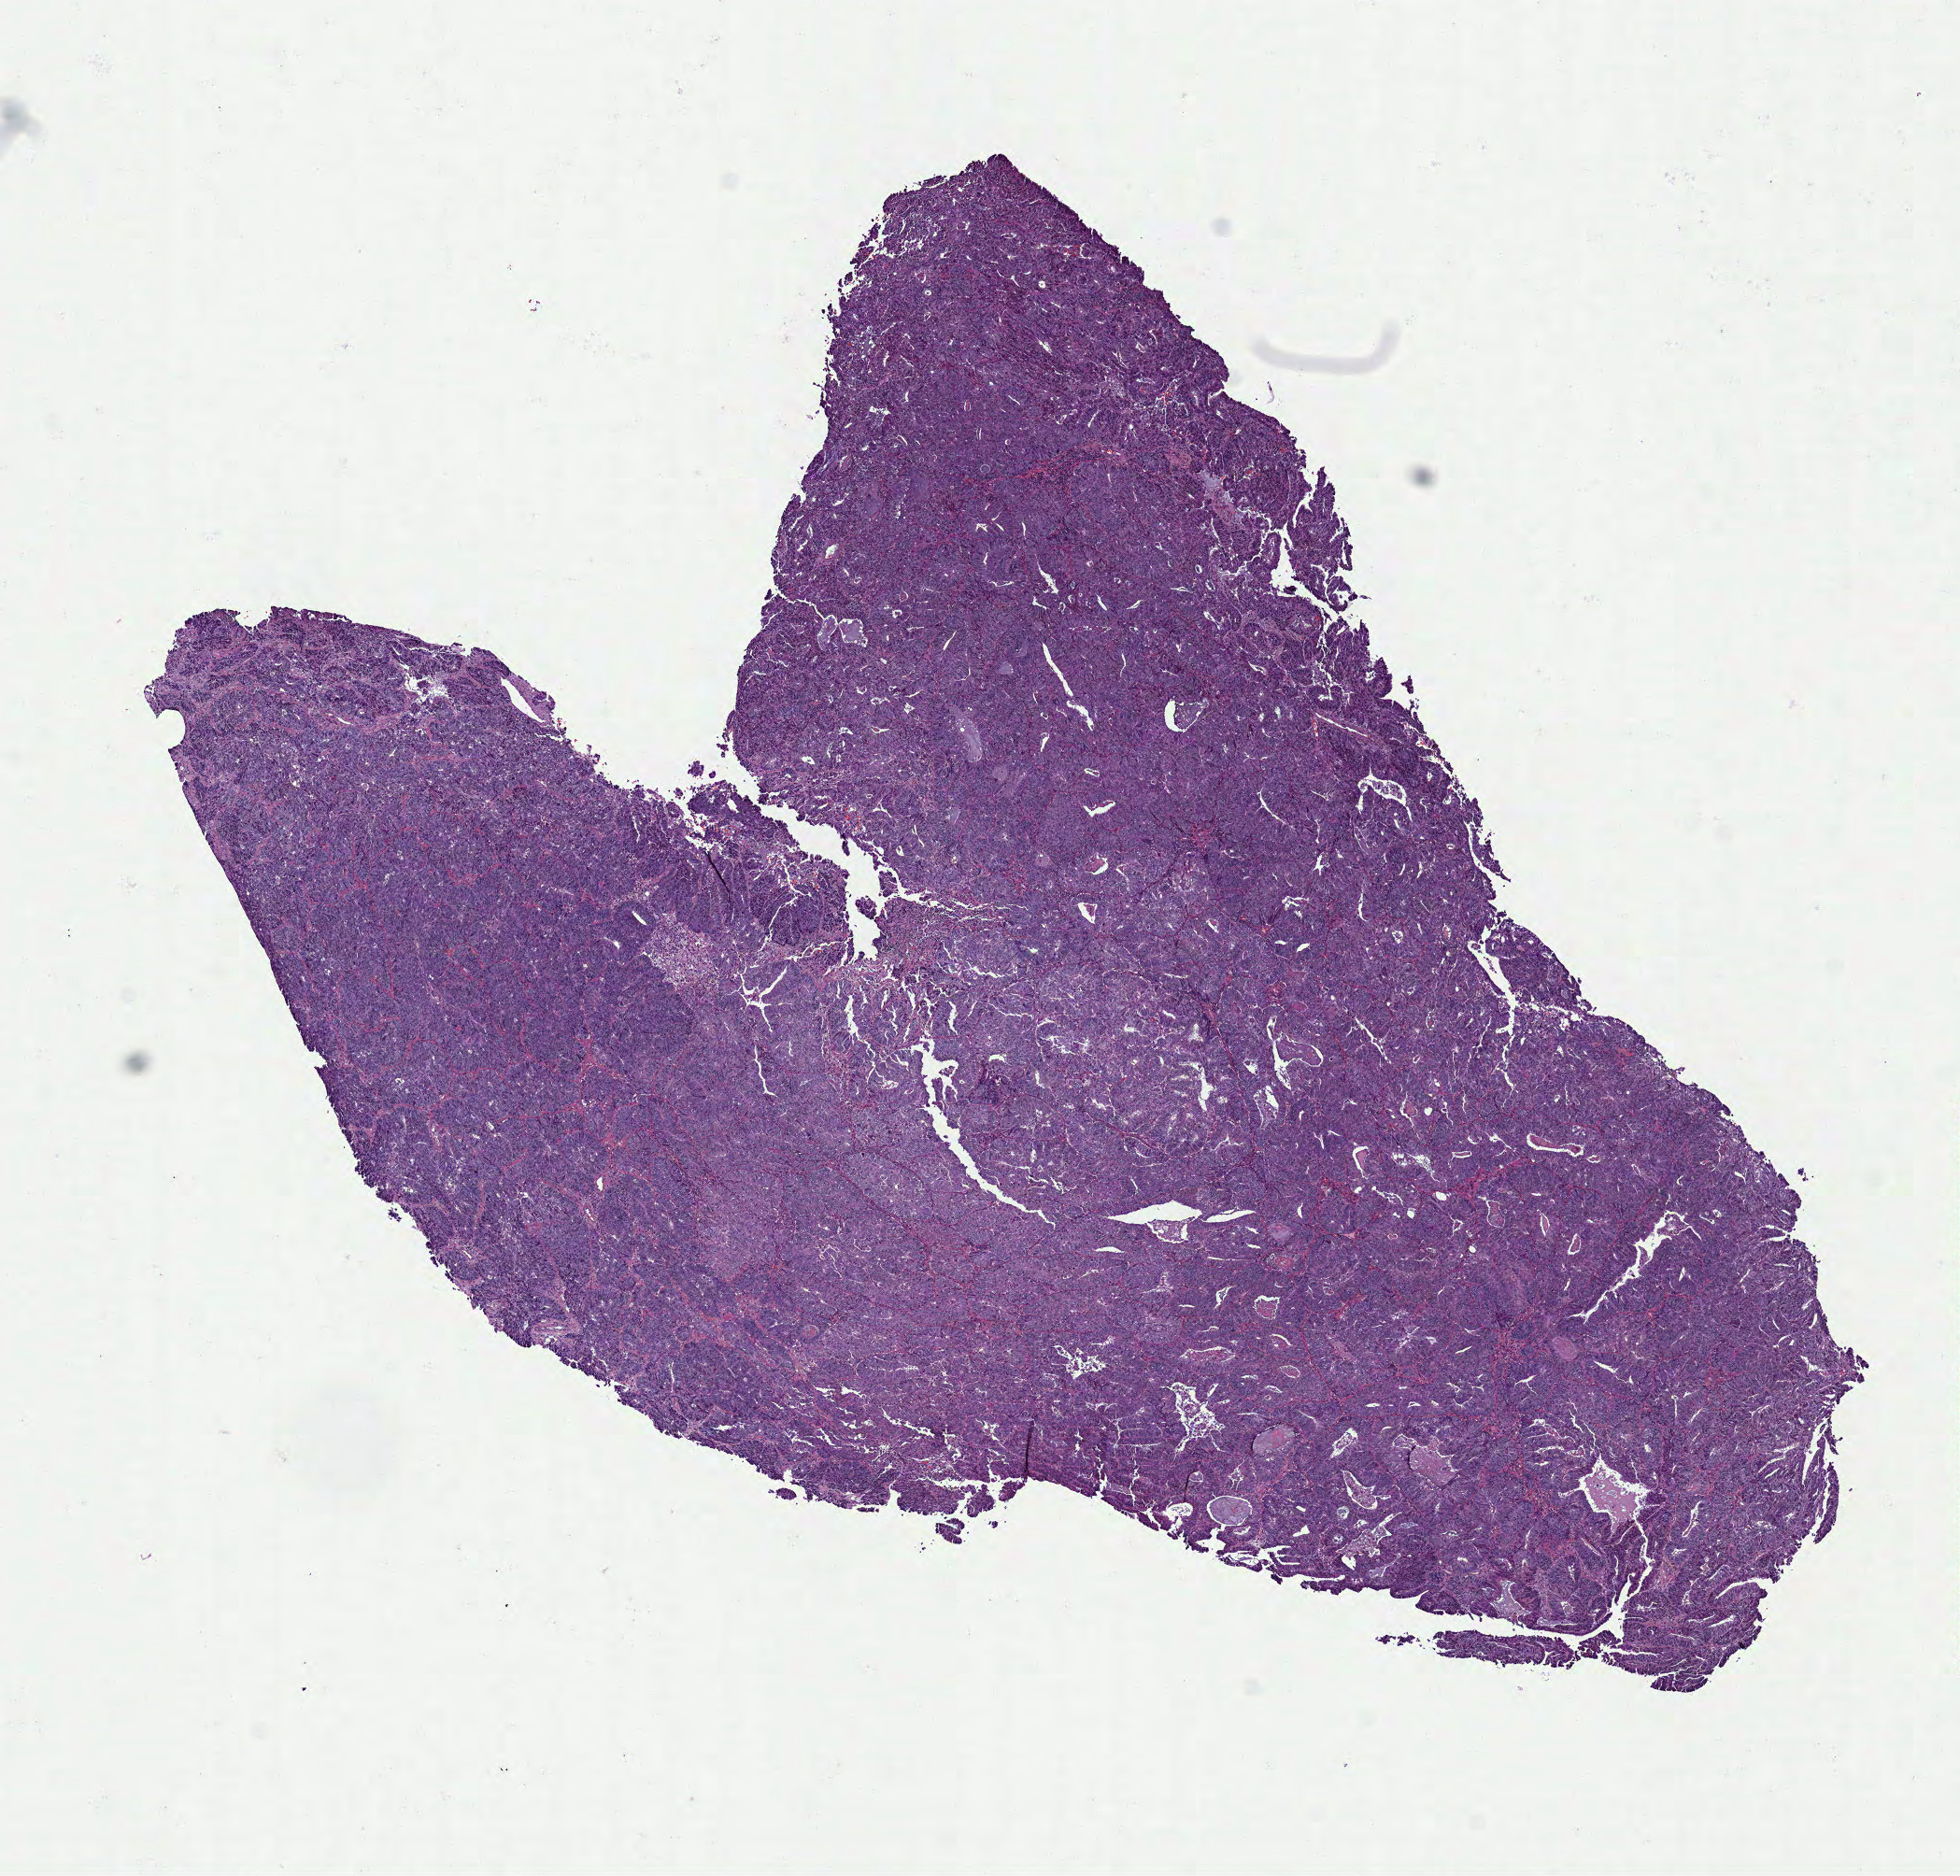
H&E-stained whole-slide image — a low-resolution overview of the entire scanned area, about 8.5 x 8.1 mm (from a 40x scan), FFPE section, primary tumour sample from the uterus. Female patient; age at initial diagnosis 64 years. Histologic grade: G2 (moderately differentiated).
Diagnosis: Endometrioid adenocarcinoma, NOS (endometrium). FIGO stage: IA.